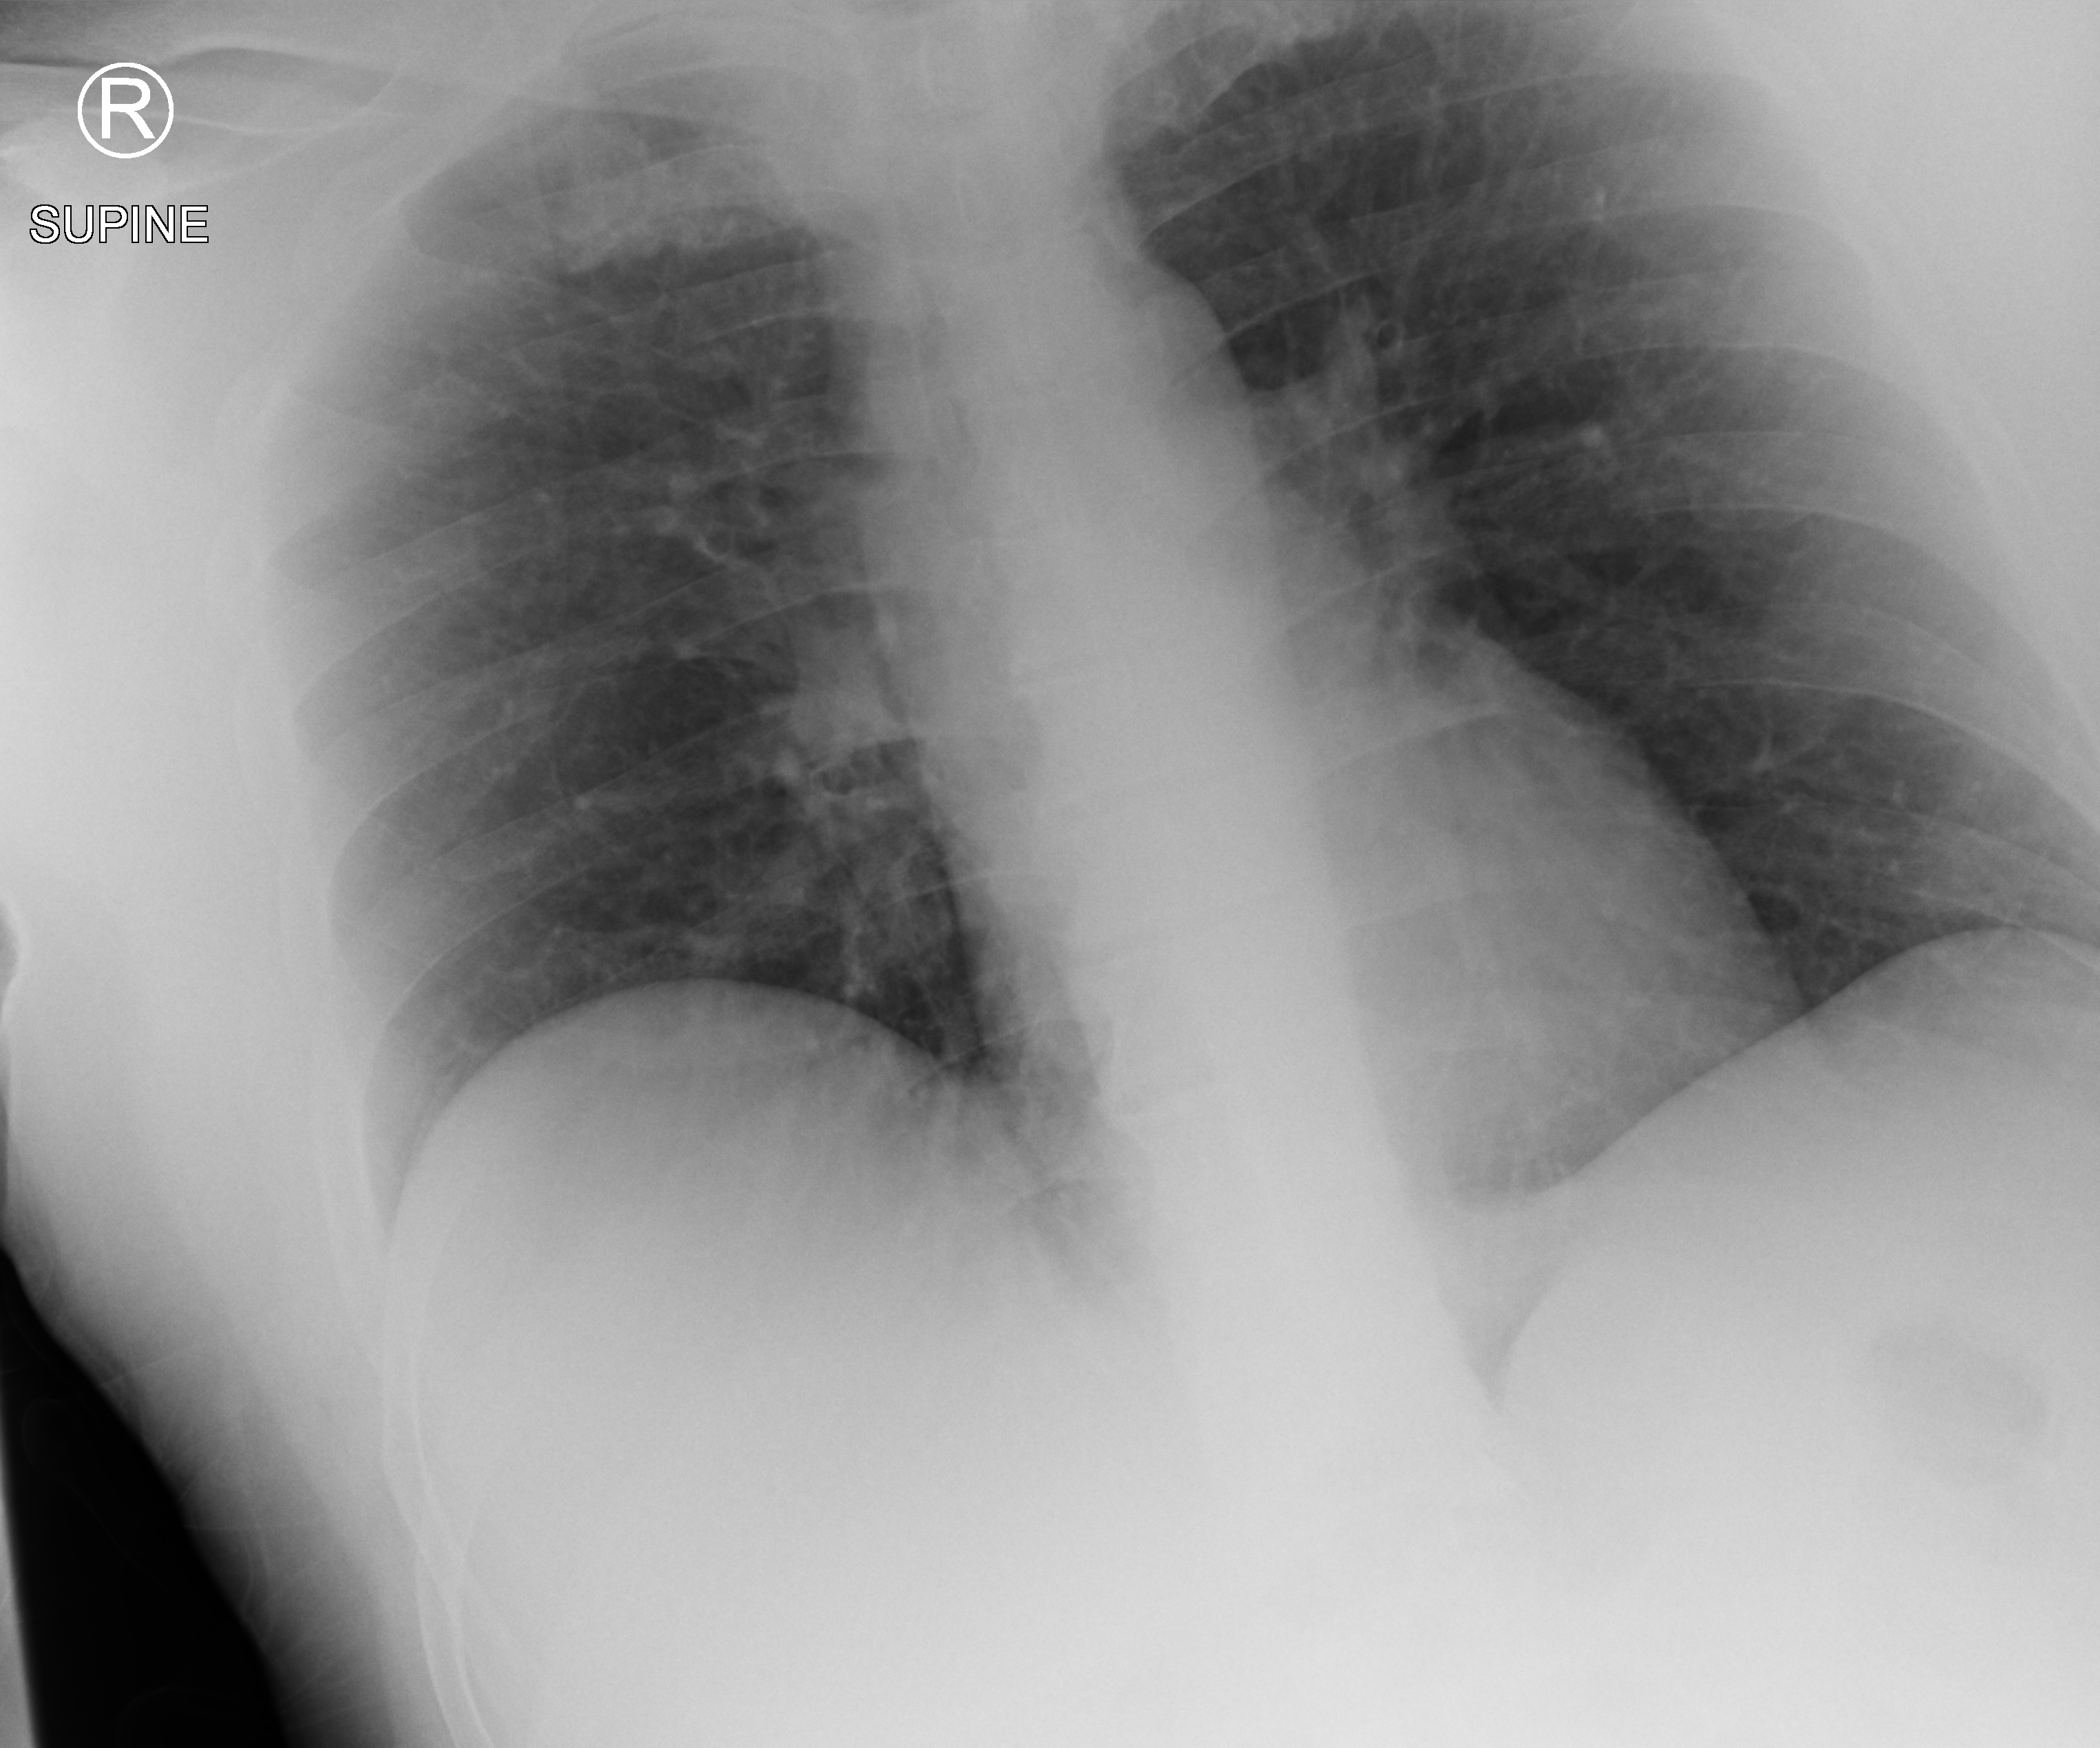
Bedside chest radiograph (computed radiography); anteroposterior (AP) projection. Male patient hospitalised with COVID-19, age 18–59 years.
Admission-level facts for this patient (not findings on this image; timing relative to this image not recorded): length of hospital stay: 2 days; admitted to intensive care during this hospital stay: no; mechanically ventilated during this hospital stay: no.